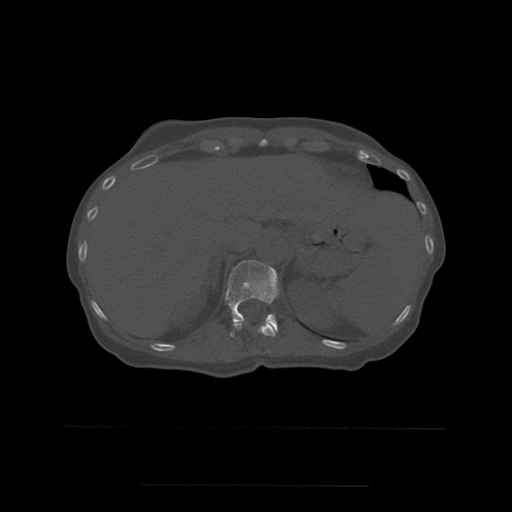
CT including the spine, one axial slice. Slice 269 of 544 in the series (ordered by position). Bone window (W 1800 / L 400 HU). 1.25 mm slice thickness. 512 × 512 image matrix, field of view 350 × 350 mm. Patient age 58 years. From the clinical record (not read from this slice): primary cancer: lung.
Outlined on this slice (semi-automatically segmented with operator editing):
- T11 vertebra: box from (x=233, y=321) to (x=276, y=337) px
- T12 vertebra: (x=225, y=260)–(x=279, y=337)